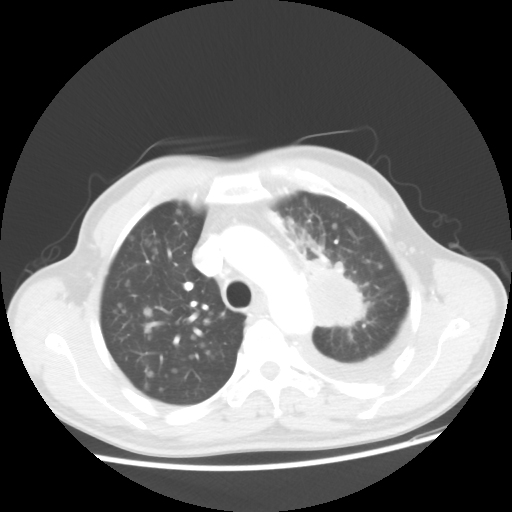
Chest CT, one axial slice; position 35 of 48 along the scan axis; reconstruction kernel STANDARD; 100 kVp; lung window (W 1500 / L -600 HU); 5 mm slice thickness; 512 × 512 image matrix. Patient: male, 55 years. Case-level facts recorded for this patient, not image findings: clinical TNM (as recorded): T2 N3 M1a.
Outlined on this slice (bounding box drawn by a radiologist):
- lung tumour (recorded histology: squamous cell carcinoma): bounding box (x1, y1, x2, y2) in pixels: (297, 250, 370, 338)